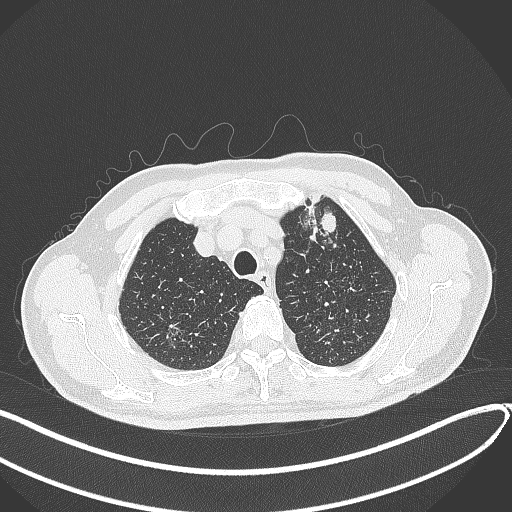
Chest CT, one axial slice; slice 352 of 459 in the series (ordered by position); reconstruction kernel B70f; lung window (W 1500 / L -600 HU); 1 mm slice thickness; 512 × 512 image matrix, field of view 400 × 400 mm. Male patient, age 74 years. From the clinical record (not read from this slice): clinical TNM (as recorded): T2b N0 M1c.
Structures marked on this image (bounding box drawn by a radiologist):
- lung tumour (recorded histology: adenocarcinoma): bounding box (x1, y1, x2, y2) in pixels: (317, 207, 339, 238)